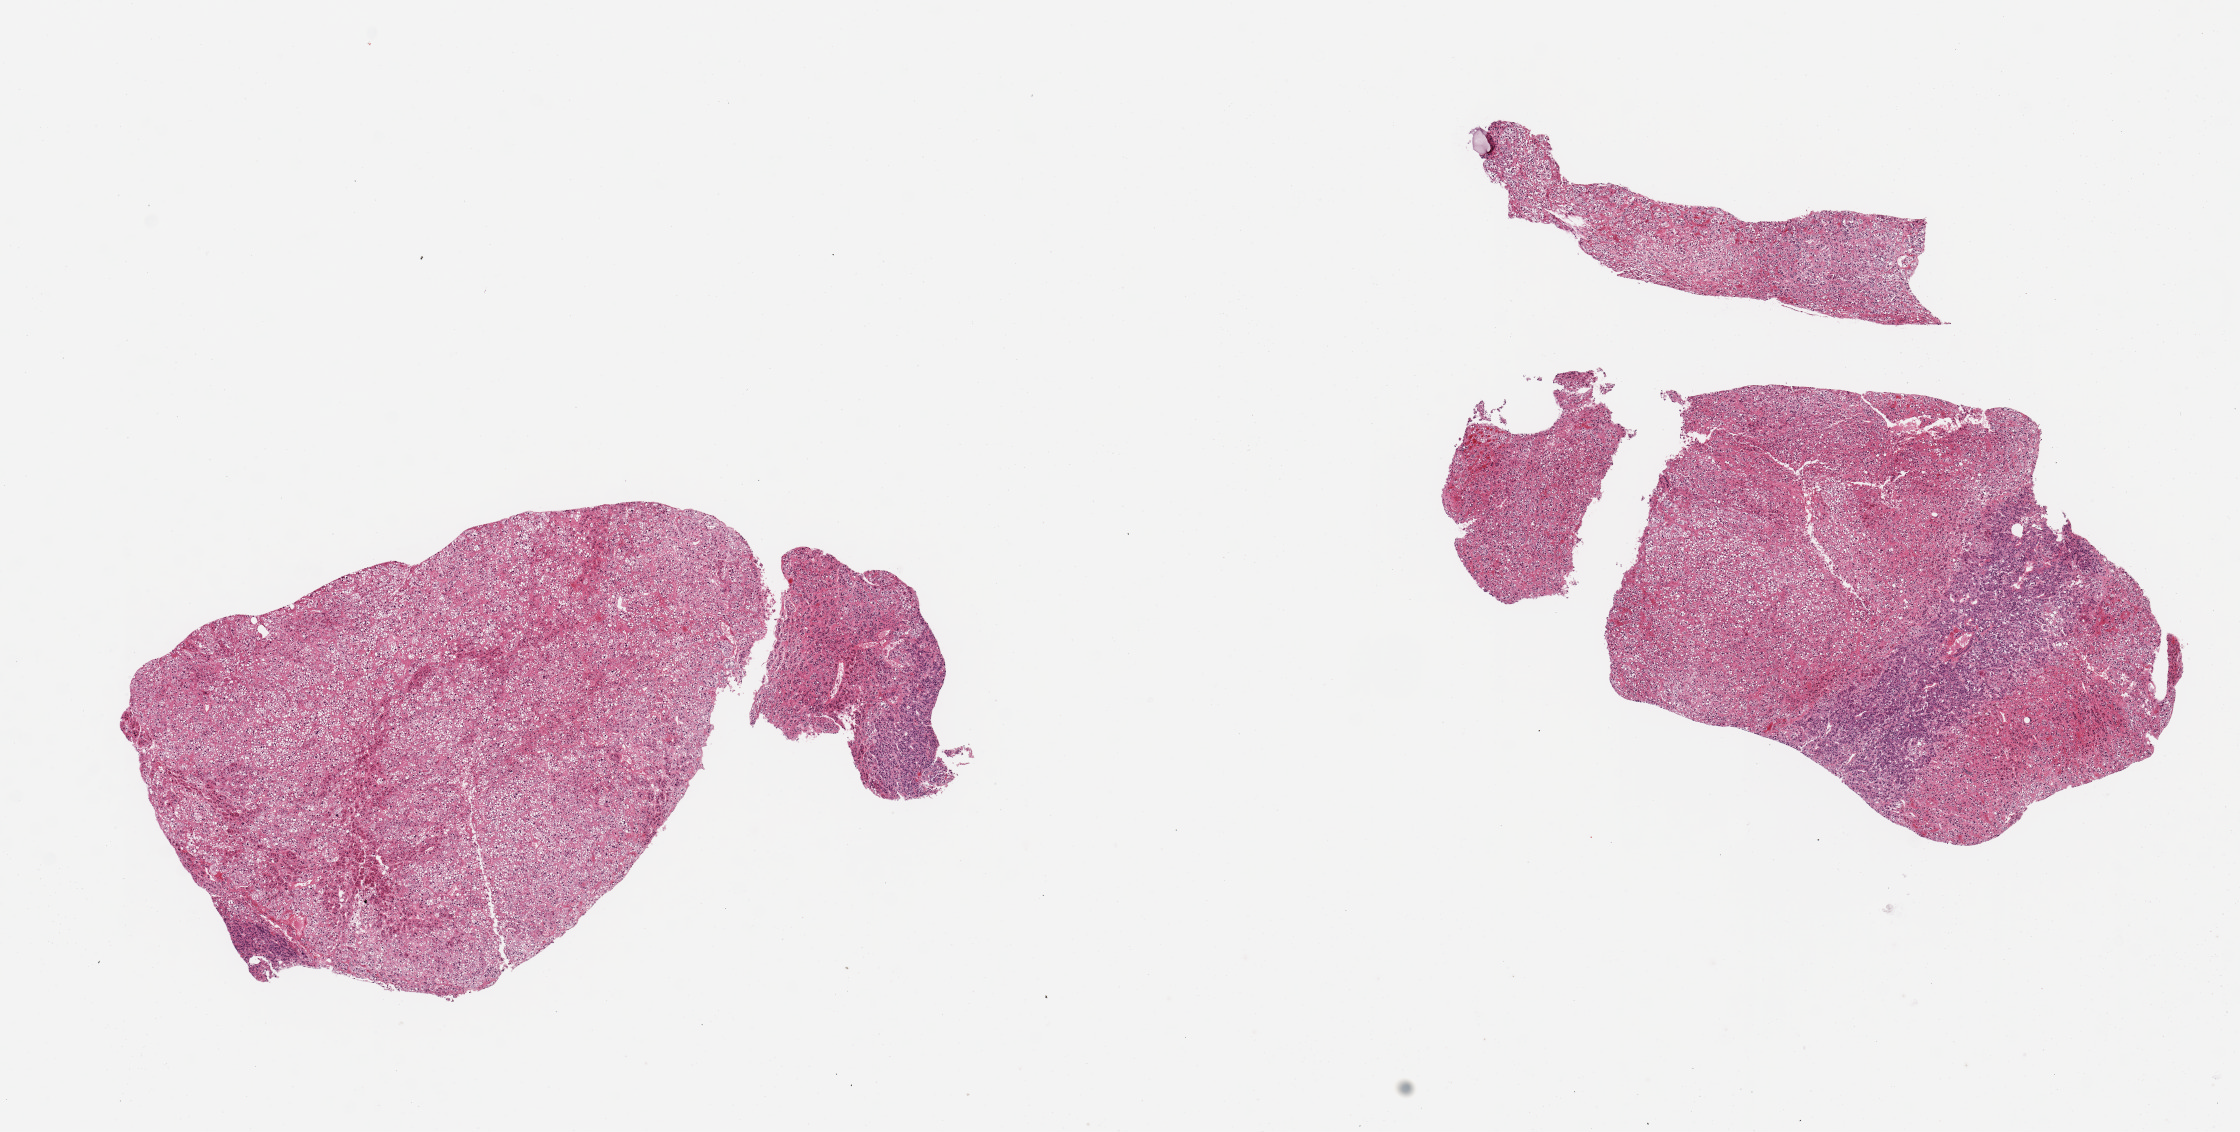
Whole-slide image, haematoxylin and eosin stain, brightfield, a low-resolution overview of the entire scanned area, about 17.7 x 9.0 mm. PAXgene-fixed paraffin-embedded (PFPE) section. Target tissue: adrenal gland. Donor tissue sample. Male donor.
Review note (as recorded): 2 pieces, mainly cortex but a ~3x0.8mm focus of medulla is present--valuable specimen, well preserved.